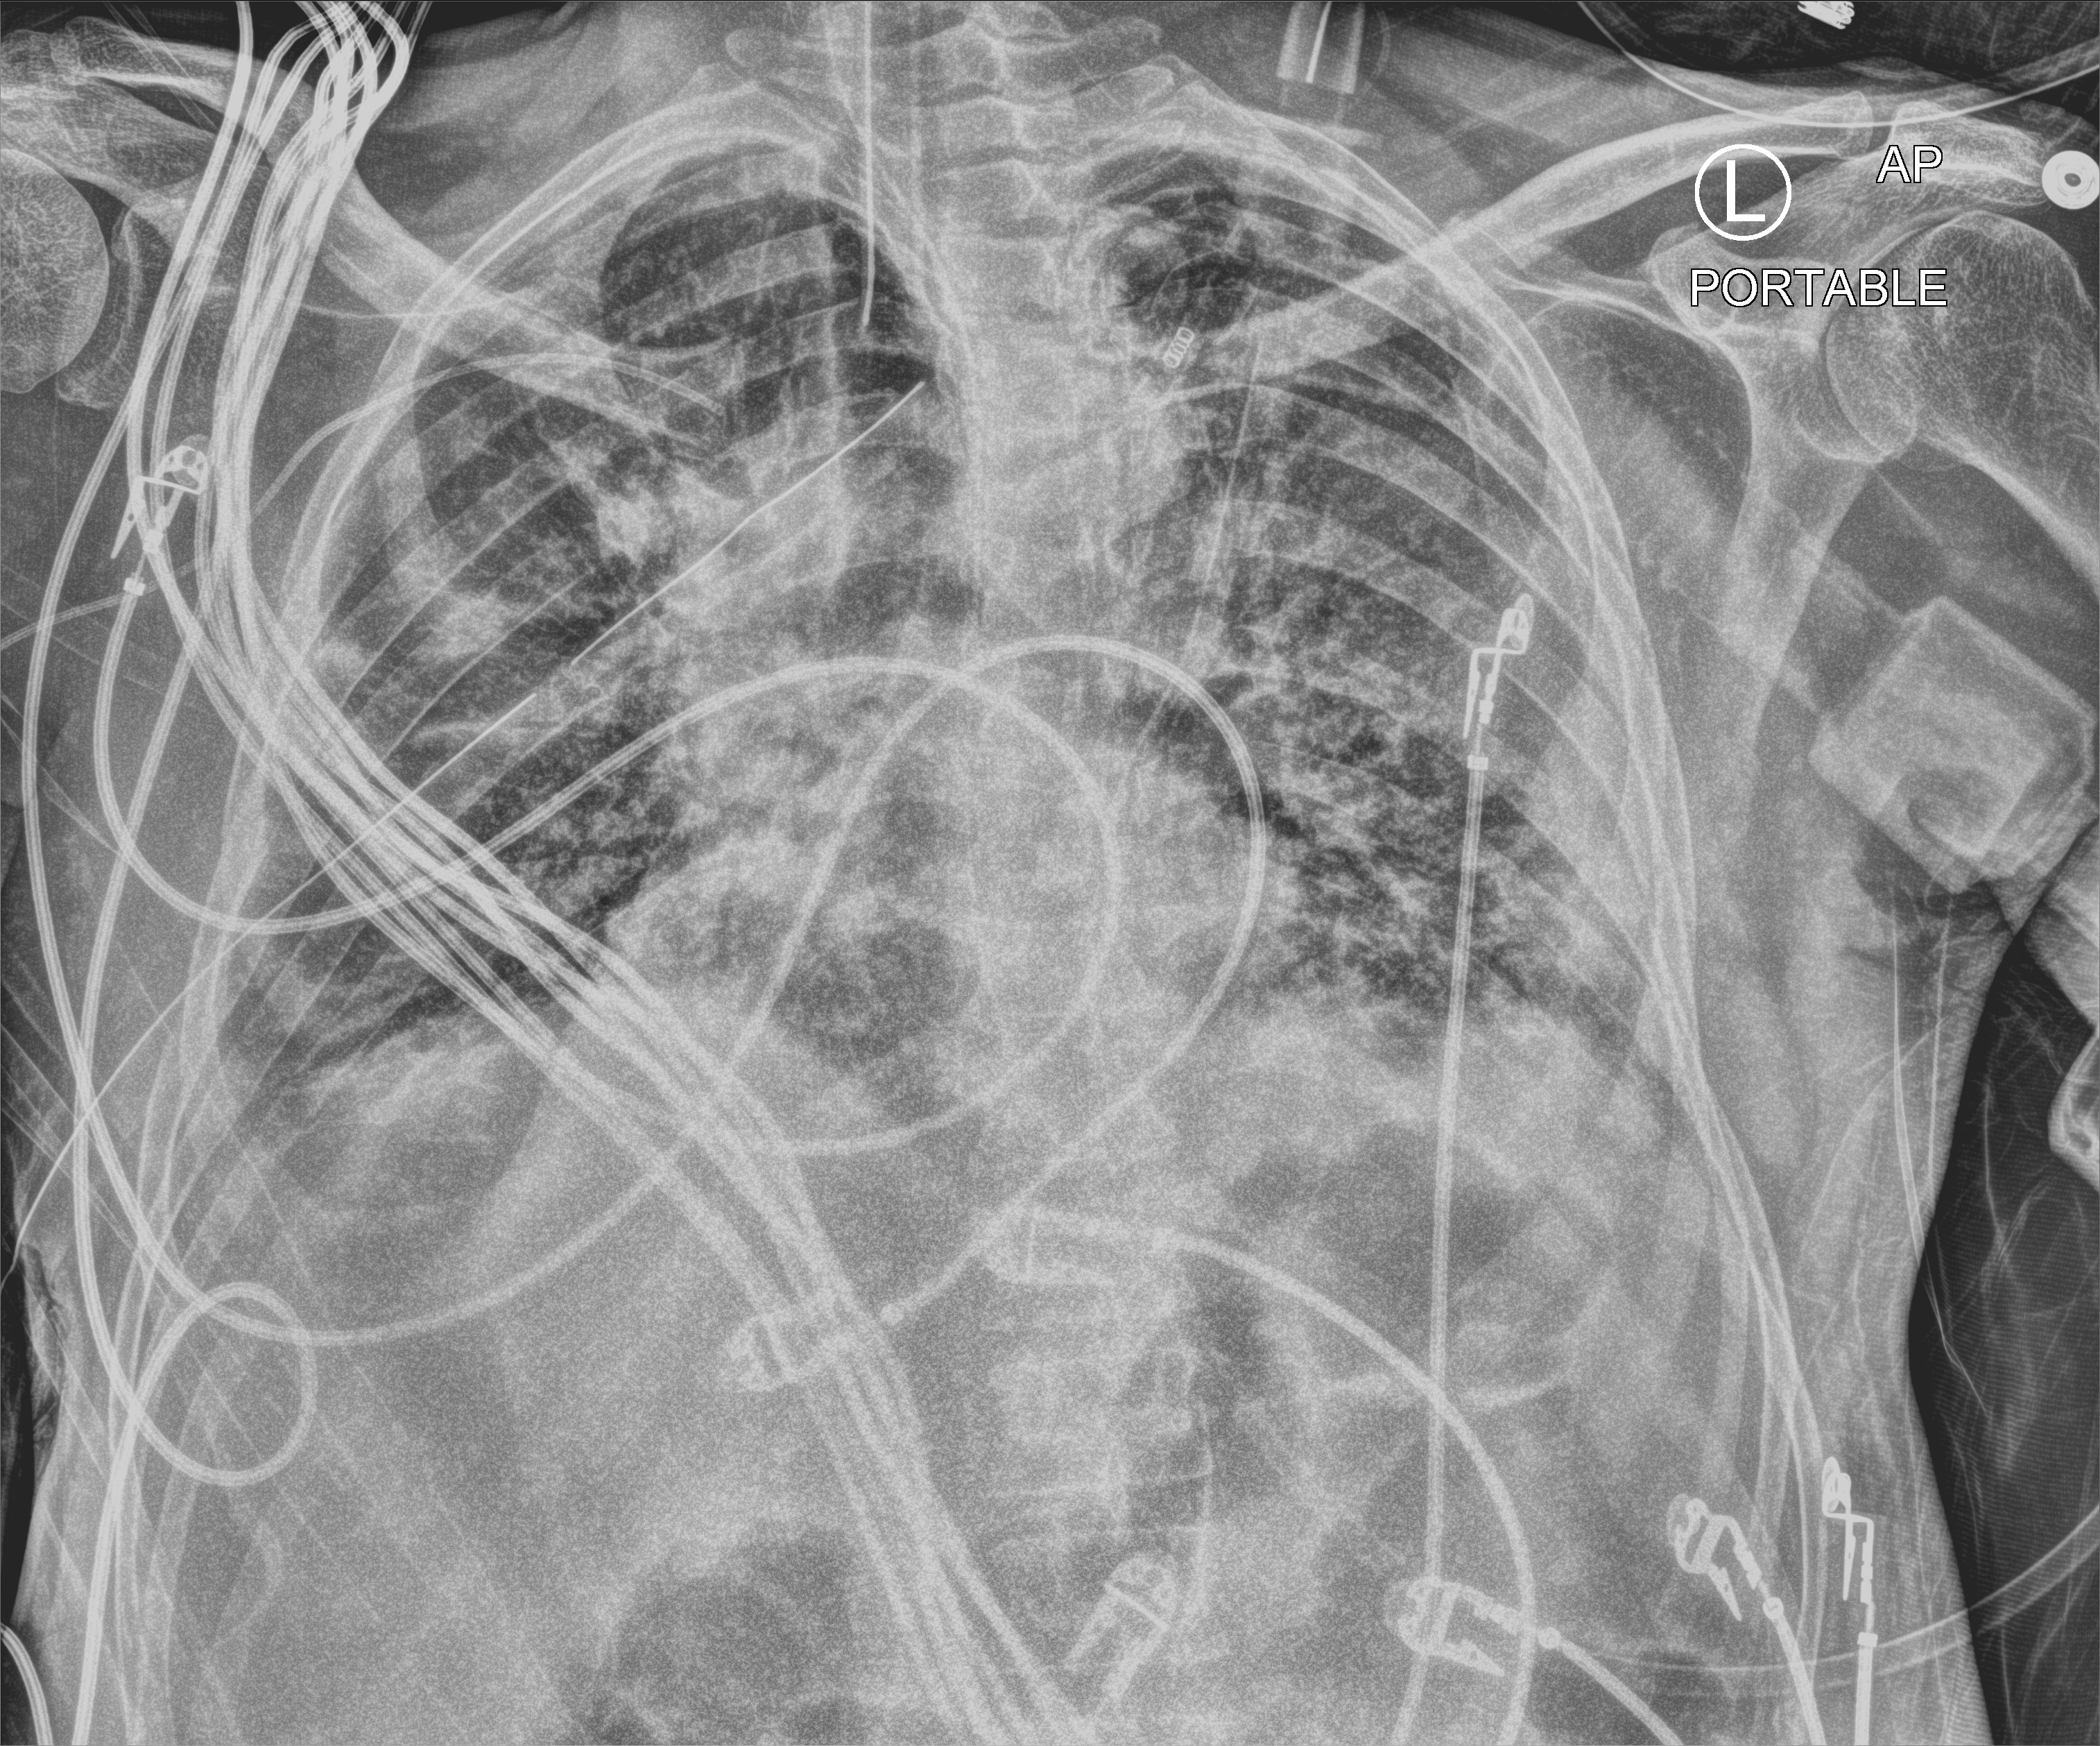
Bedside chest radiograph (computed radiography); anteroposterior (AP) projection. Male patient hospitalised with COVID-19, age 18–59 years.
Hospital-stay facts (about this admission, not read from this image; timing relative to this image not recorded):
- mechanically ventilated during this hospital stay: yes
- admitted to intensive care during this hospital stay: yes